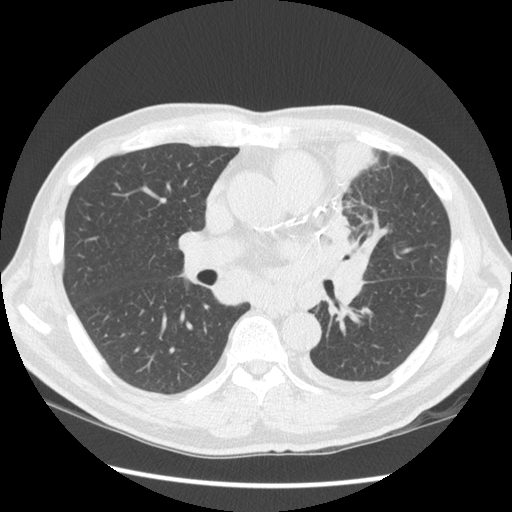
Low-dose screening chest CT, one axial slice. Slice 78 of 136 in the series (ordered by position). Reconstruction kernel STANDARD. Lung window (W 1500 / L -600 HU). 2.5 mm slice thickness. 512 × 512 image matrix.
Annotated regions visible in this slice (manually delineated by an expert):
- lesion 1 (tumor, upper lobe of left lung): bounding box (x1, y1, x2, y2) in pixels: (322, 141, 374, 264)